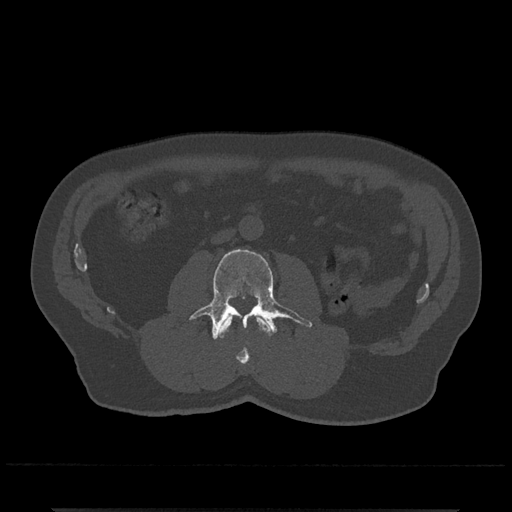
CT including the spine, one axial slice; position 235 of 797 along the scan axis; reconstruction kernel Br40s/3; bone window (W 1800 / L 400 HU); 0.5 mm slice thickness; 512 × 512 image matrix, field of view 393 × 393 mm. Patient: male, 67 years. Case-level facts recorded for this patient, not image findings: primary cancer: prostate.
Annotated regions visible in this slice (semi-automatically segmented with operator editing):
- L2 vertebra: bounding box (x1, y1, x2, y2) in pixels: (218, 315, 271, 365)
- L3 vertebra: (190, 249, 313, 340)